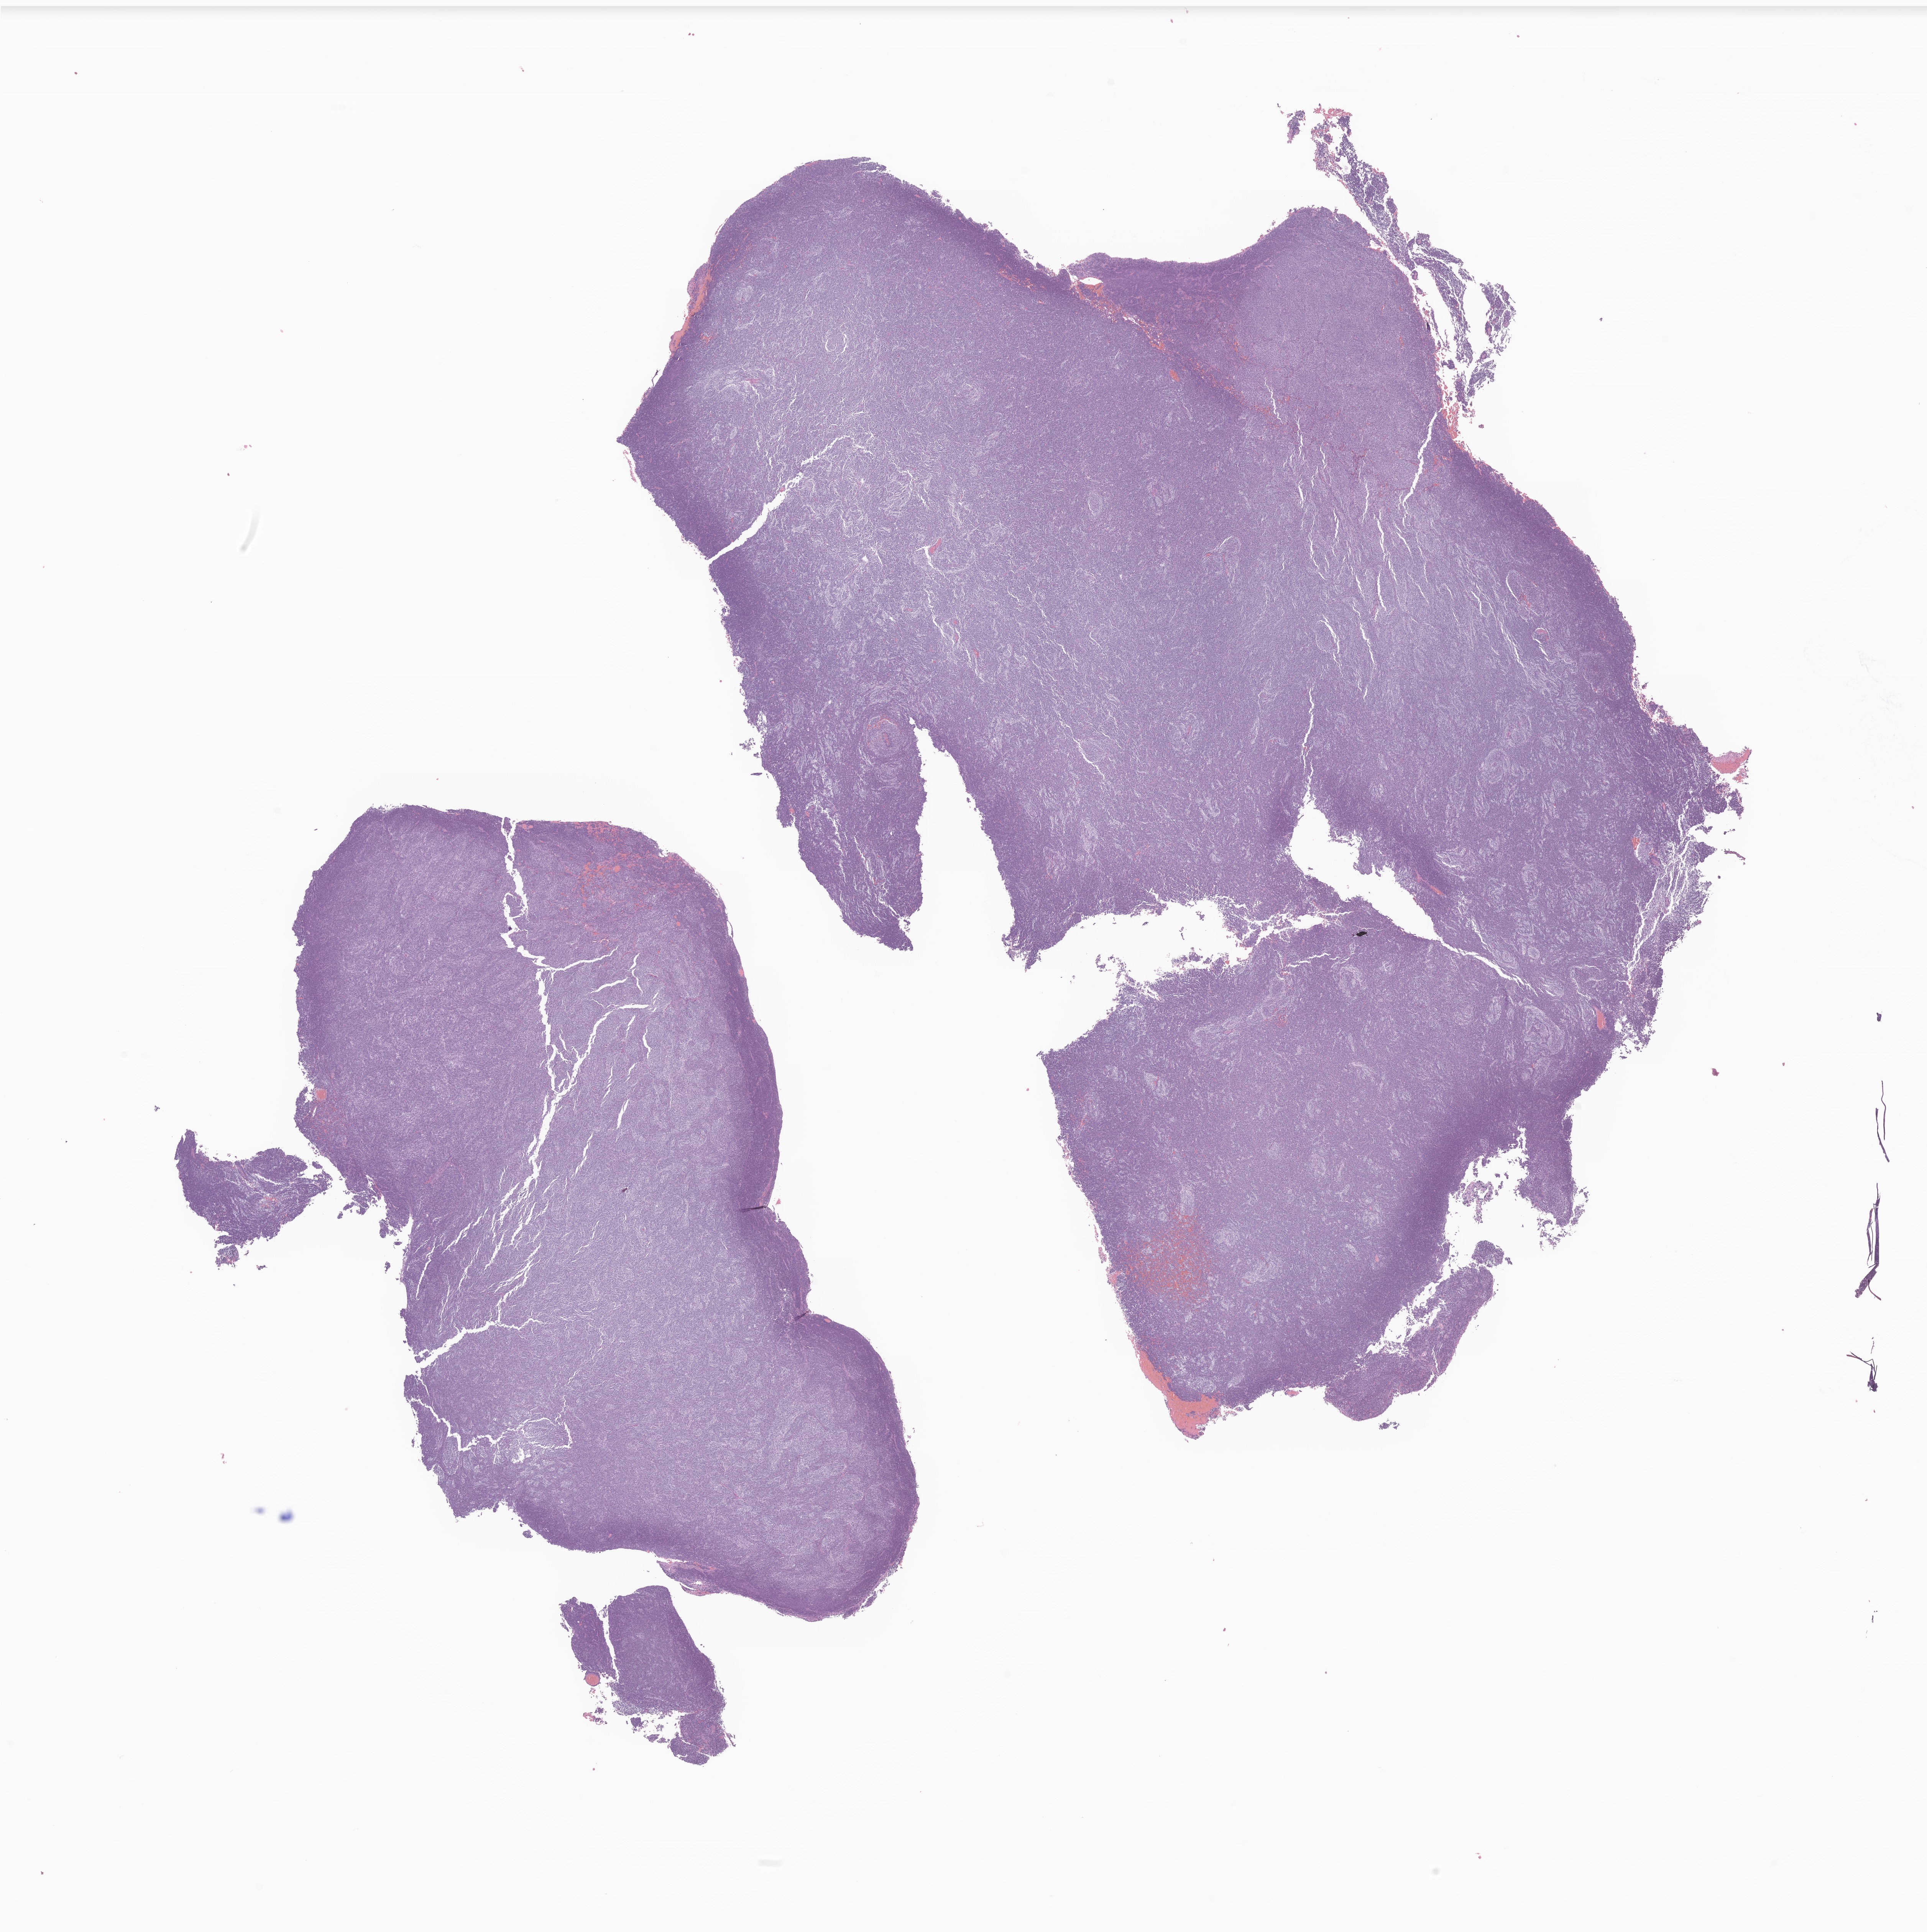
Whole-slide image, haematoxylin and eosin stain of tumor tissue from the cerebellum, shown as a low-resolution overview of the whole scanned area (about 21.2 x 21.2 mm), formalin-fixed paraffin-embedded section. Patient: female, age 217 months.
Diagnosis (ICD-O-3 morphology term): Medulloblastoma, NOS.